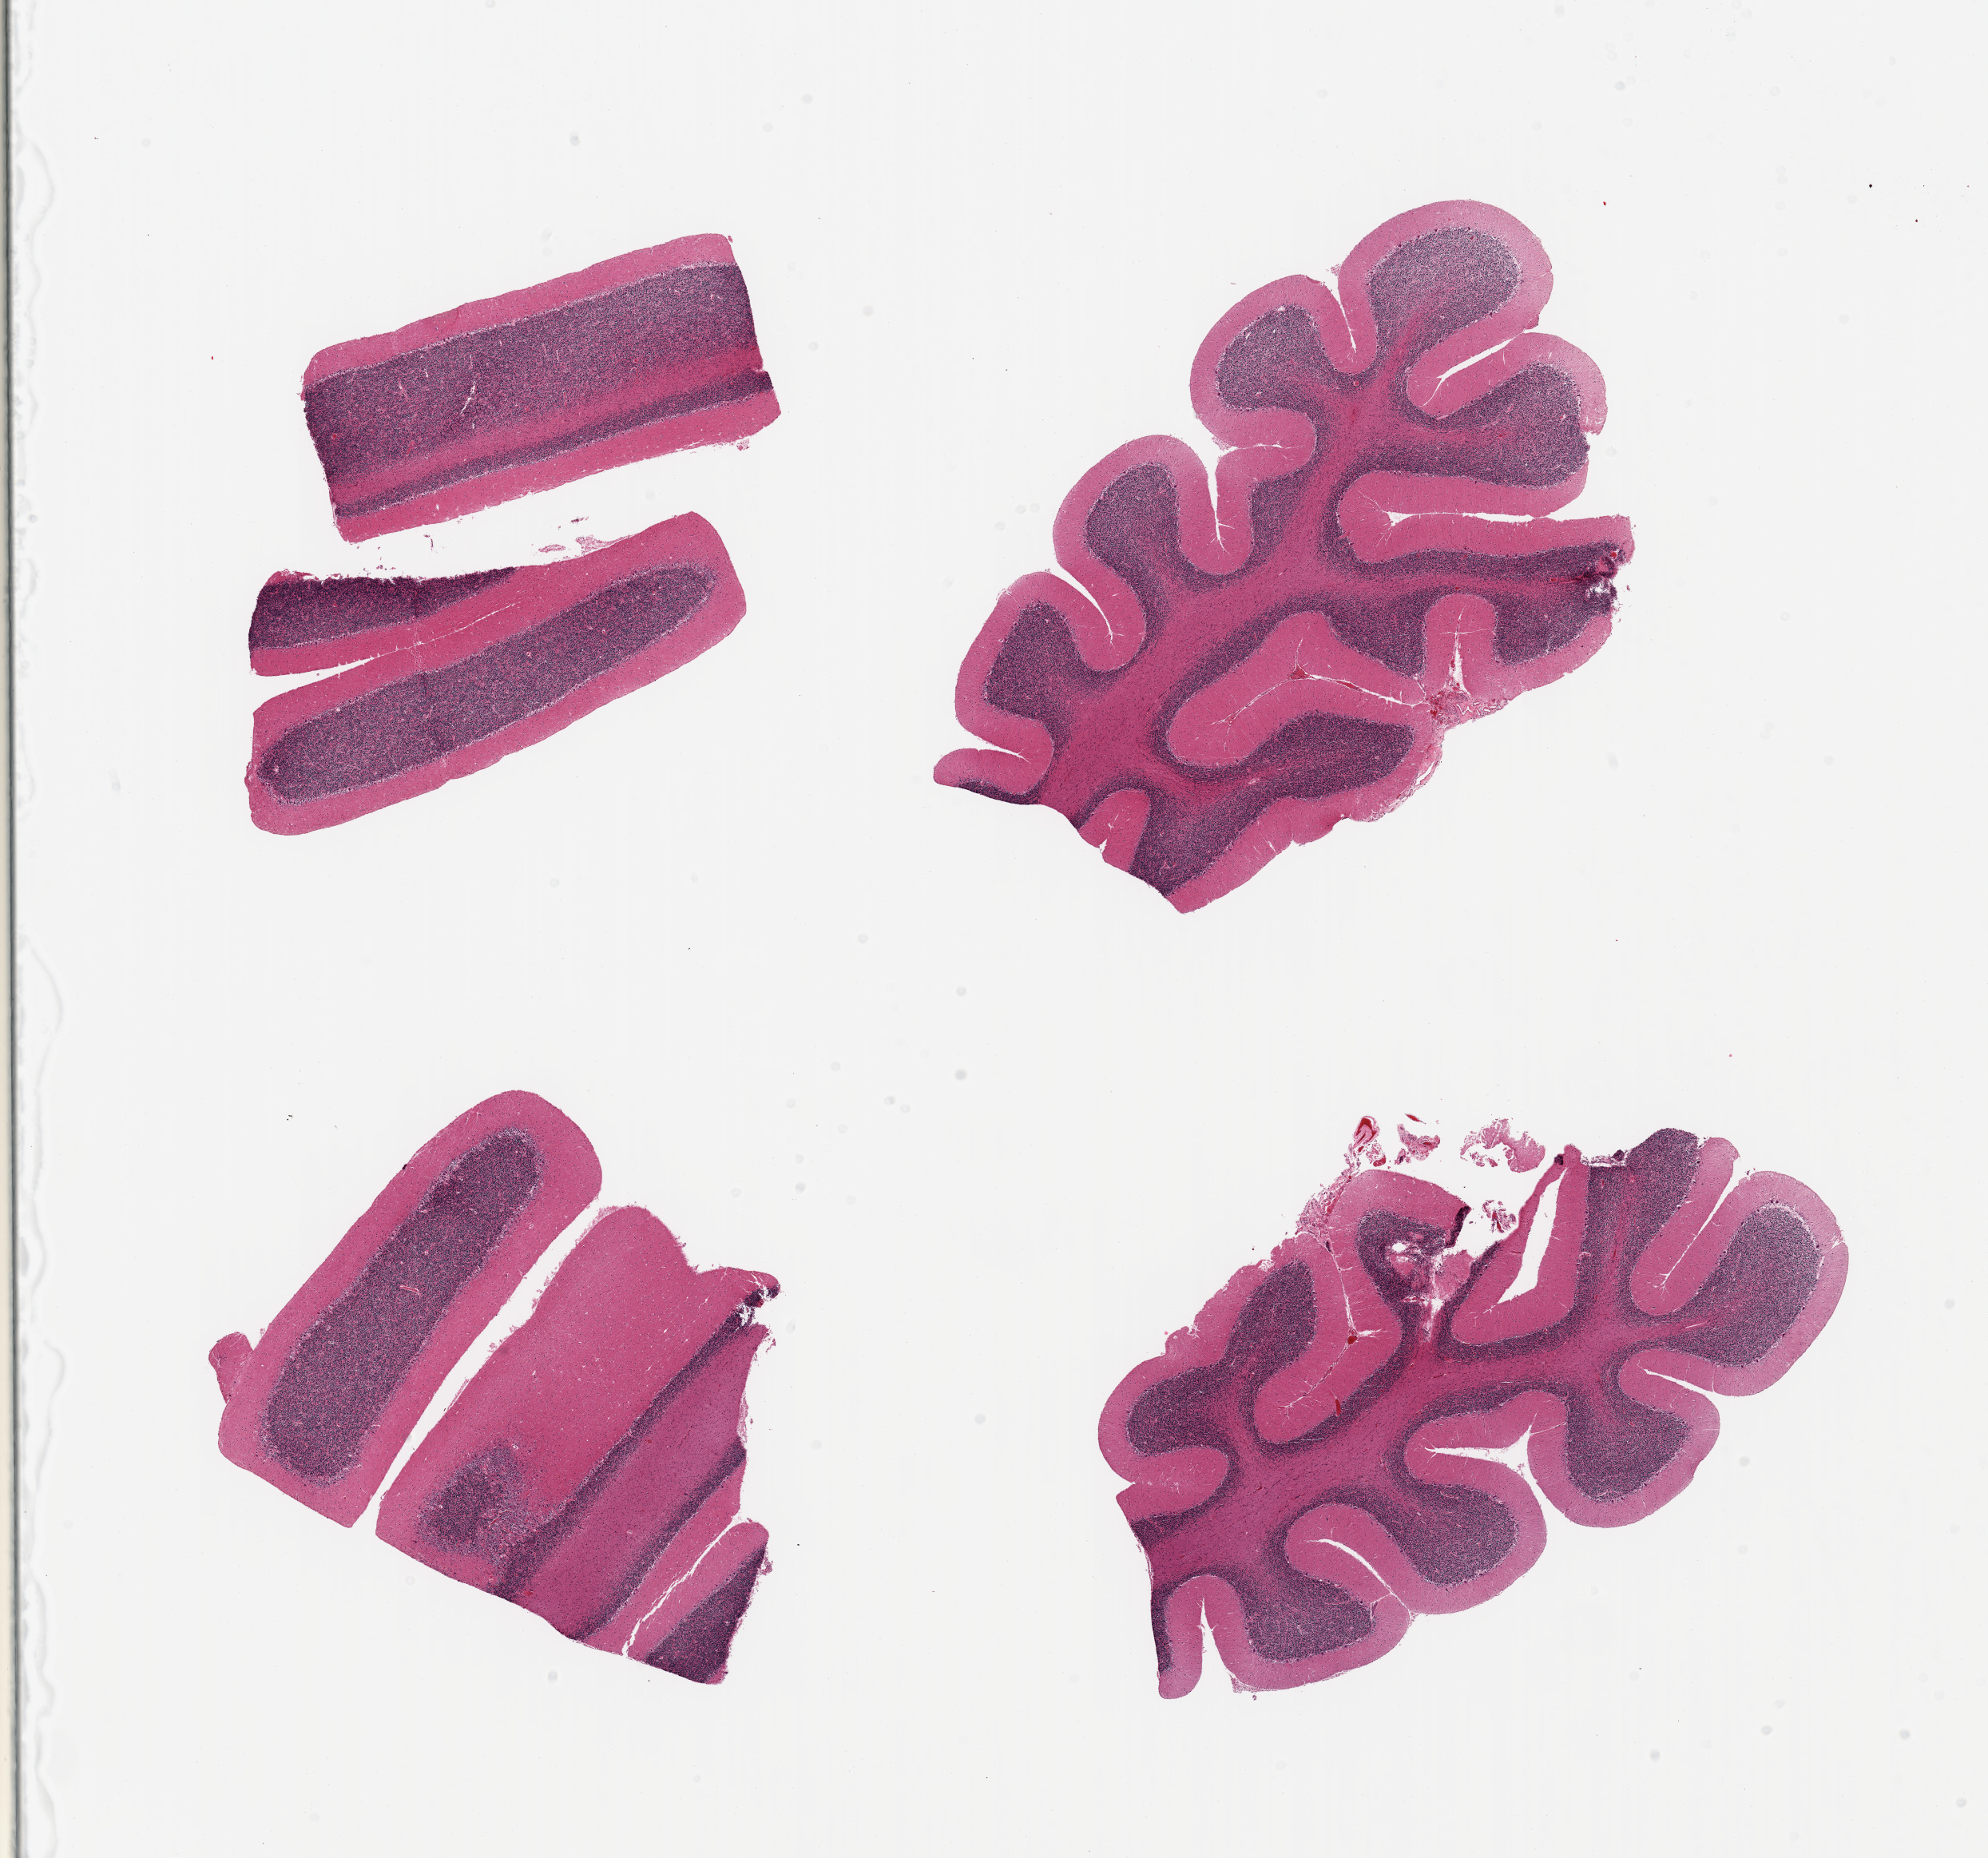
Digitized haematoxylin and eosin-stained section, whole scanned area (about 19.7 x 18.4 mm) shown as a low-resolution overview; PAXgene-fixed paraffin-embedded (PFPE) section; target tissue: cerebellum; tissue donor sample. Male donor.
Pathologist's review note for this sample: 4 pieces; Purkinje cells well visualized.